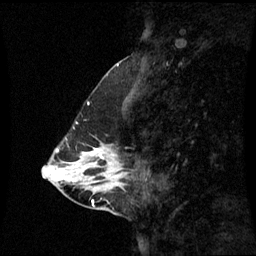
Breast MRI (dynamic contrast-enhanced), one sagittal slice. Position 24 of 60 along the scan axis. Dynamic contrast-enhanced series, image 2 of 3 at this slice position (ordered by acquisition). 1.5 T. TE 4.2 ms, TR 8.9 ms. 2.3 mm slice thickness. 256 × 256 image matrix, field of view 240 × 240 mm. Patient: female, 43 years. Case-level facts recorded for this patient, not image findings: setting: breast cancer imaged before/during neoadjuvant chemotherapy; receptor status: HR-positive, HER2-negative.
Annotated regions visible in this slice (semi-automatically segmented with operator editing):
- analysis volume of interest (the breast-tissue region the enhancement analysis was run in; not a lesion): box from (x=78, y=144) to (x=127, y=193) px
- tumour enhancement mask (voxels above the 70 % enhancement threshold inside the analysis volume of interest): (x=91, y=148)–(x=99, y=153)